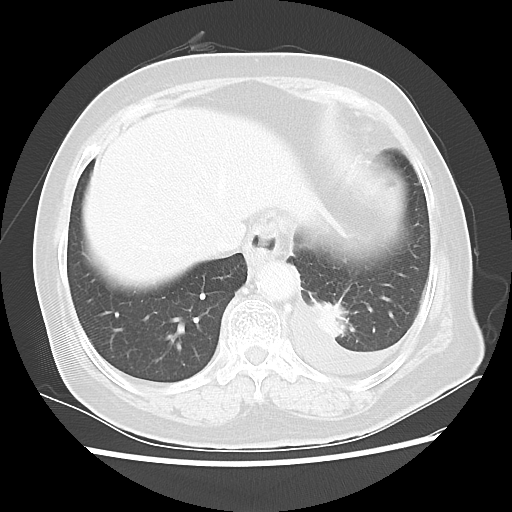
Chest CT, one axial slice; reconstruction kernel LUNG; 100 kVp; lung window (W 1500 / L -600 HU); 512 × 512 image matrix, field of view 343 × 343 mm. Female patient, age 68 years. From the clinical record (not read from this slice): clinical TNM (as recorded): T1c N0 M1.
Outlined on this slice (bounding box drawn by a radiologist):
- lung tumour (recorded histology: adenocarcinoma): bounding box (x1, y1, x2, y2) in pixels: (311, 297, 356, 344)